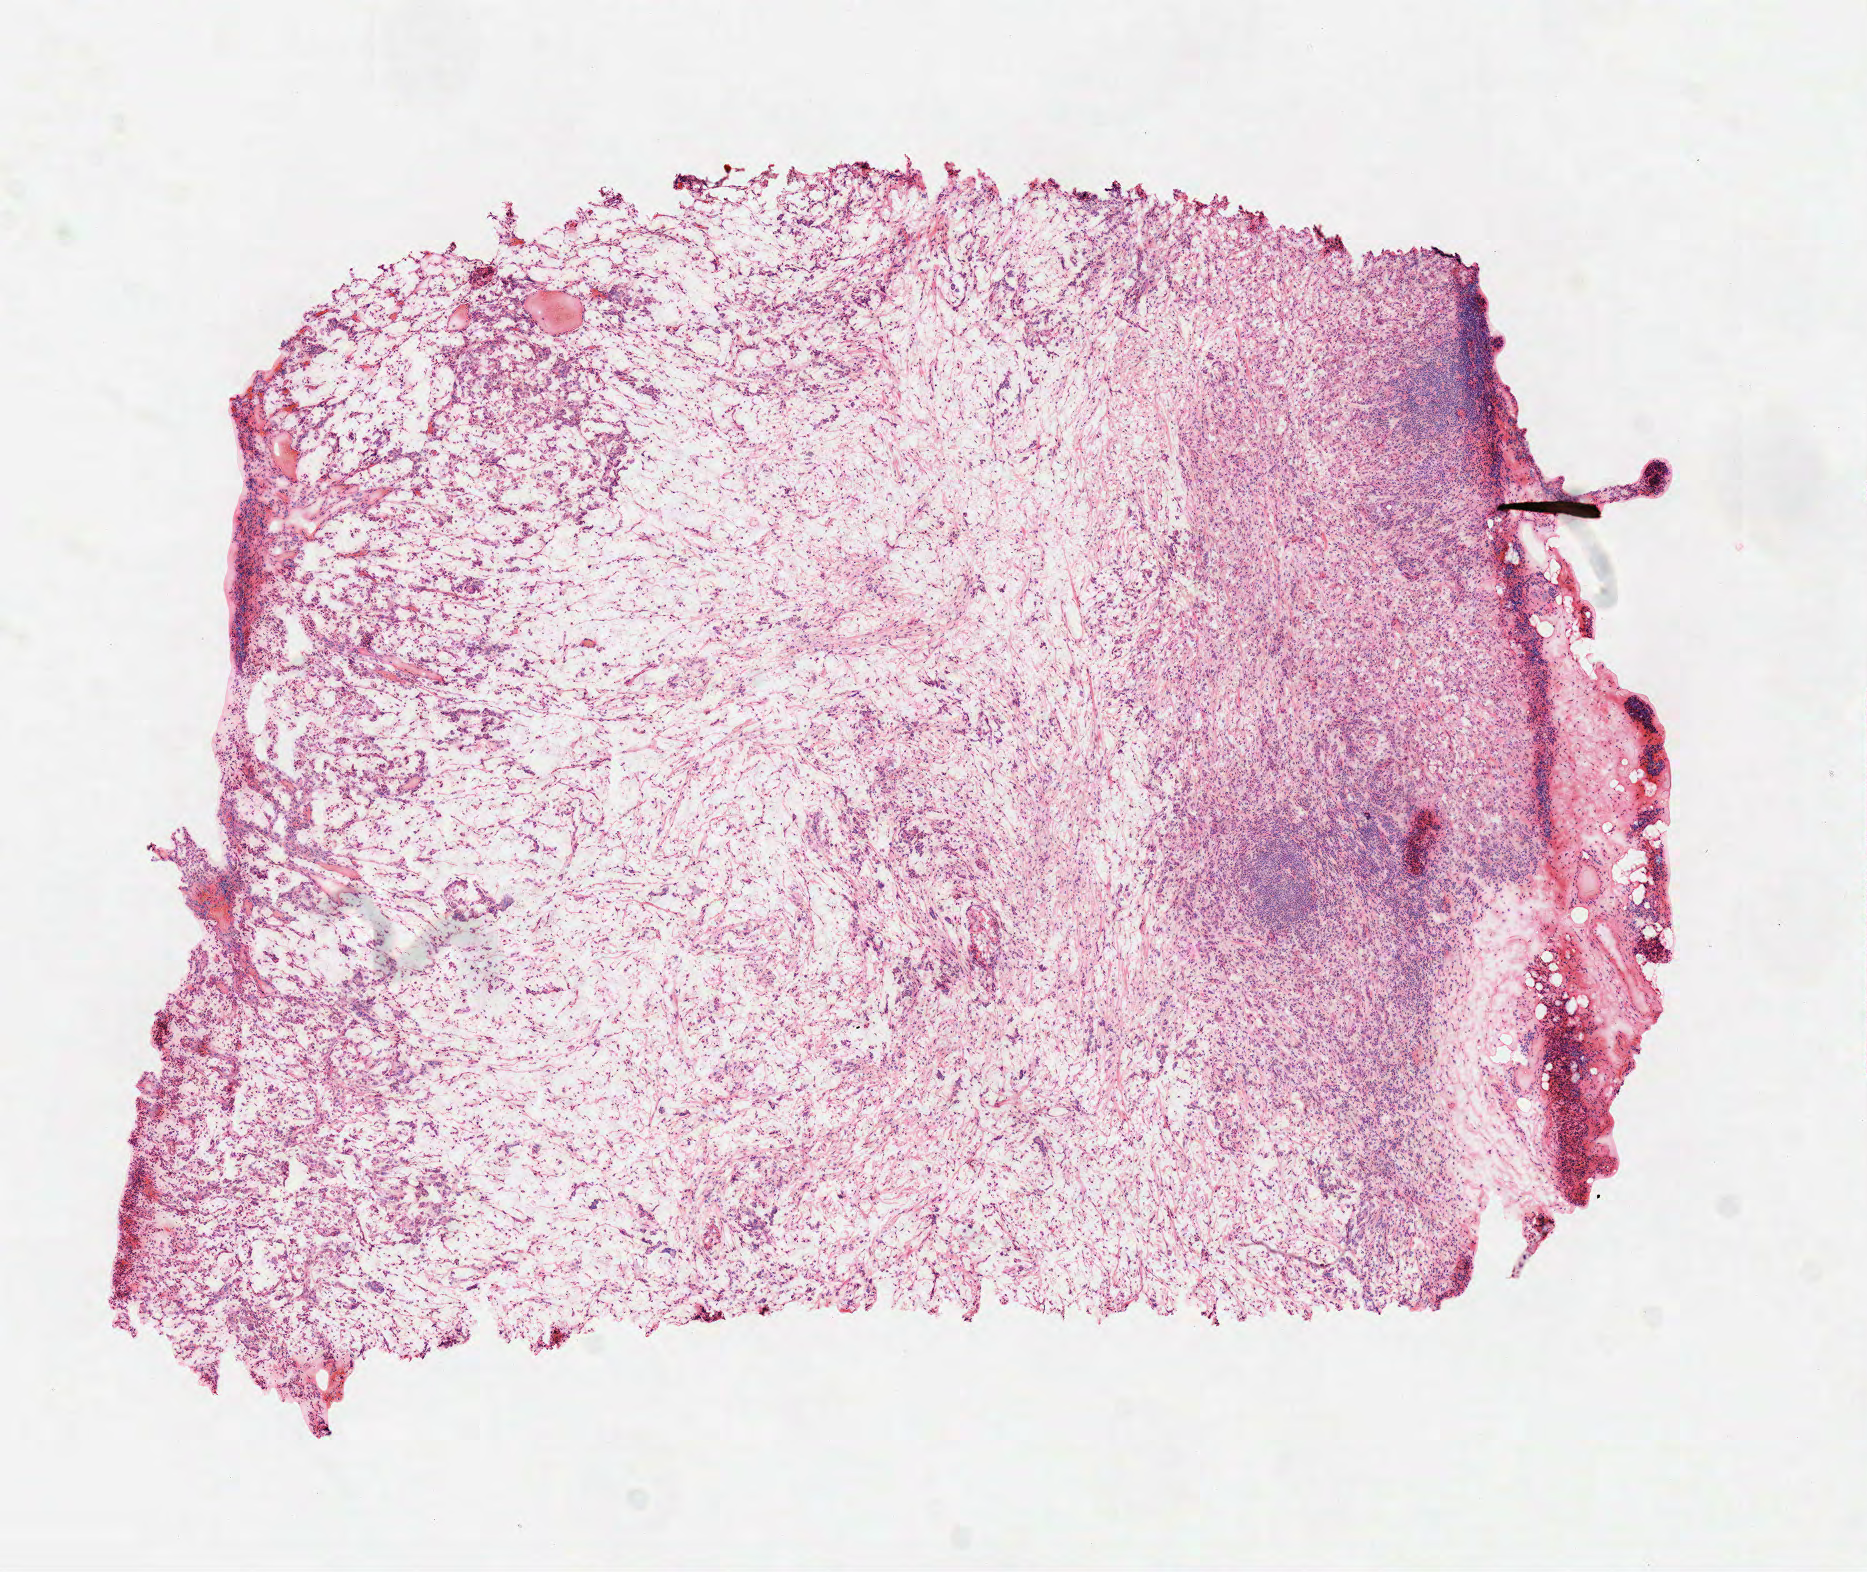
H&E-stained whole-slide image — a low-resolution overview of the entire scanned area, about 7.3 x 6.2 mm (from a 40x scan). Frozen section. Stomach, primary tumour sample. Male, age 58 years at initial diagnosis. Slide review estimates, as recorded: tumour cells 50%, tumour nuclei 65%.
Diagnosis: Carcinoma, diffuse type.